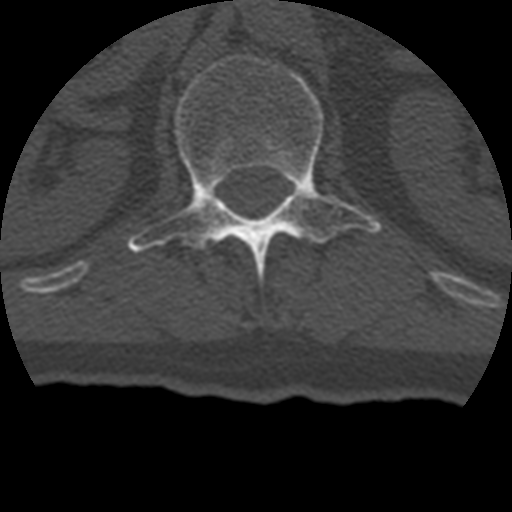
CT including the spine, one axial slice. Reconstruction kernel STANDARD. 120 kVp. Bone window (W 1800 / L 400 HU). 512 × 512 image matrix. Patient age 69 years. Case-level facts recorded for this patient, not image findings: primary cancer: prostate.
Annotated regions visible in this slice (semi-automatic segmentation, software-assisted and operator-edited):
- L1 vertebra: bounding box <127,53,382,276> (left, top, right, bottom; pixels)